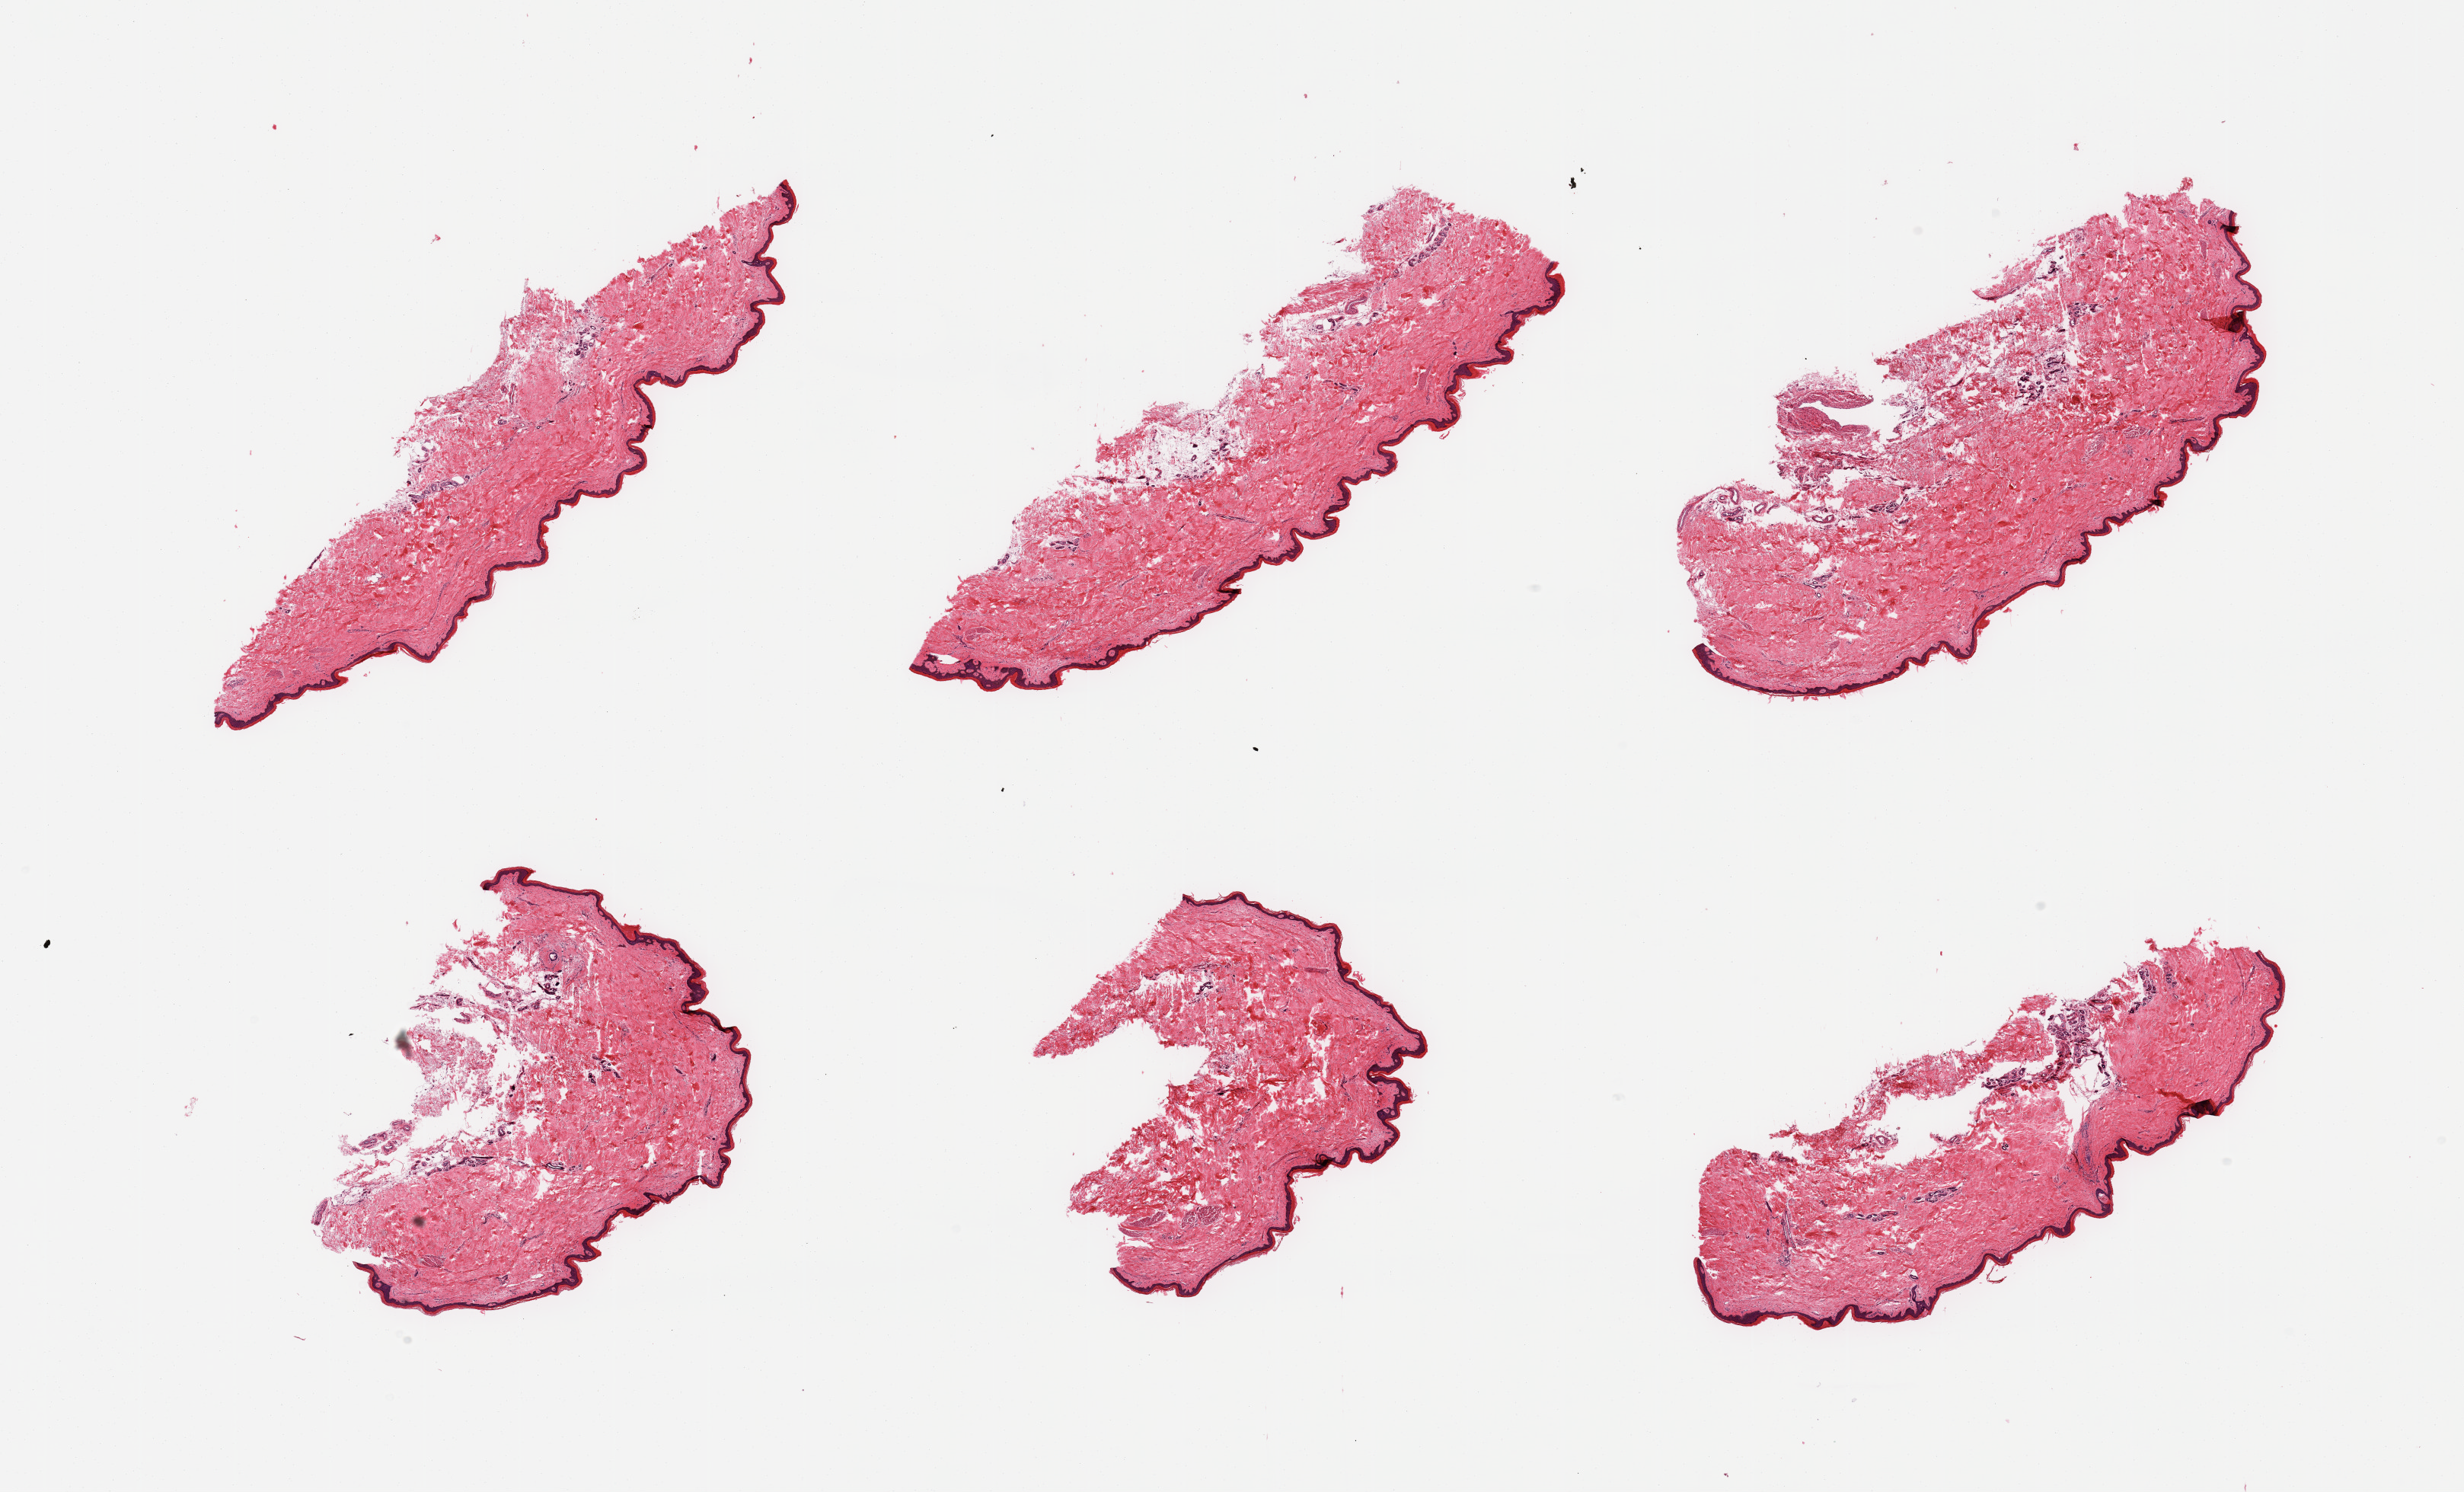
Whole-slide image, haematoxylin and eosin stain — low-resolution overview of the scanned area, about 25.6 x 15.5 mm. PAXgene-fixed paraffin-embedded (PFPE) section. Sampled site (target tissue): skin of lower leg. Donor tissue sample. Female donor.
Reviewer comment on this tissue sample: 6 pieces; well trimmed, well preserved.